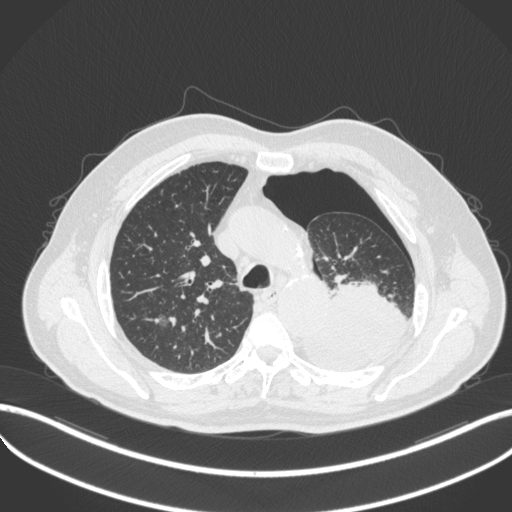
Chest CT, one axial slice. Position 368 of 466 along the scan axis. Reconstruction kernel B31f. 120 kVp. Lung window (W 1500 / L -600 HU). 1 mm slice thickness. 512 × 512 image matrix. Patient: male, 76 years. From the clinical record (not read from this slice): clinical TNM (as recorded): T3 N0 M1b.
Outlined on this slice (rectangle marked by the reading radiologist):
- lung tumour (recorded histology: adenocarcinoma): bounding box (x1, y1, x2, y2) in pixels: (308, 278, 413, 368)